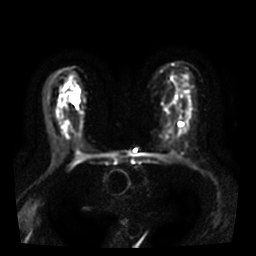
Breast MRI, one axial slice; position 20 of 38 along the scan axis; diffusion-weighted series; image 2 of 4 stored at this slice position (different b-values; order by instance number); 3 T; 256 × 256 image matrix. Female patient.
Annotated regions visible in this slice (outlined manually by an expert reader):
- tumour on diffusion-weighted imaging: bounding box <72,90,78,106> (left, top, right, bottom; pixels)